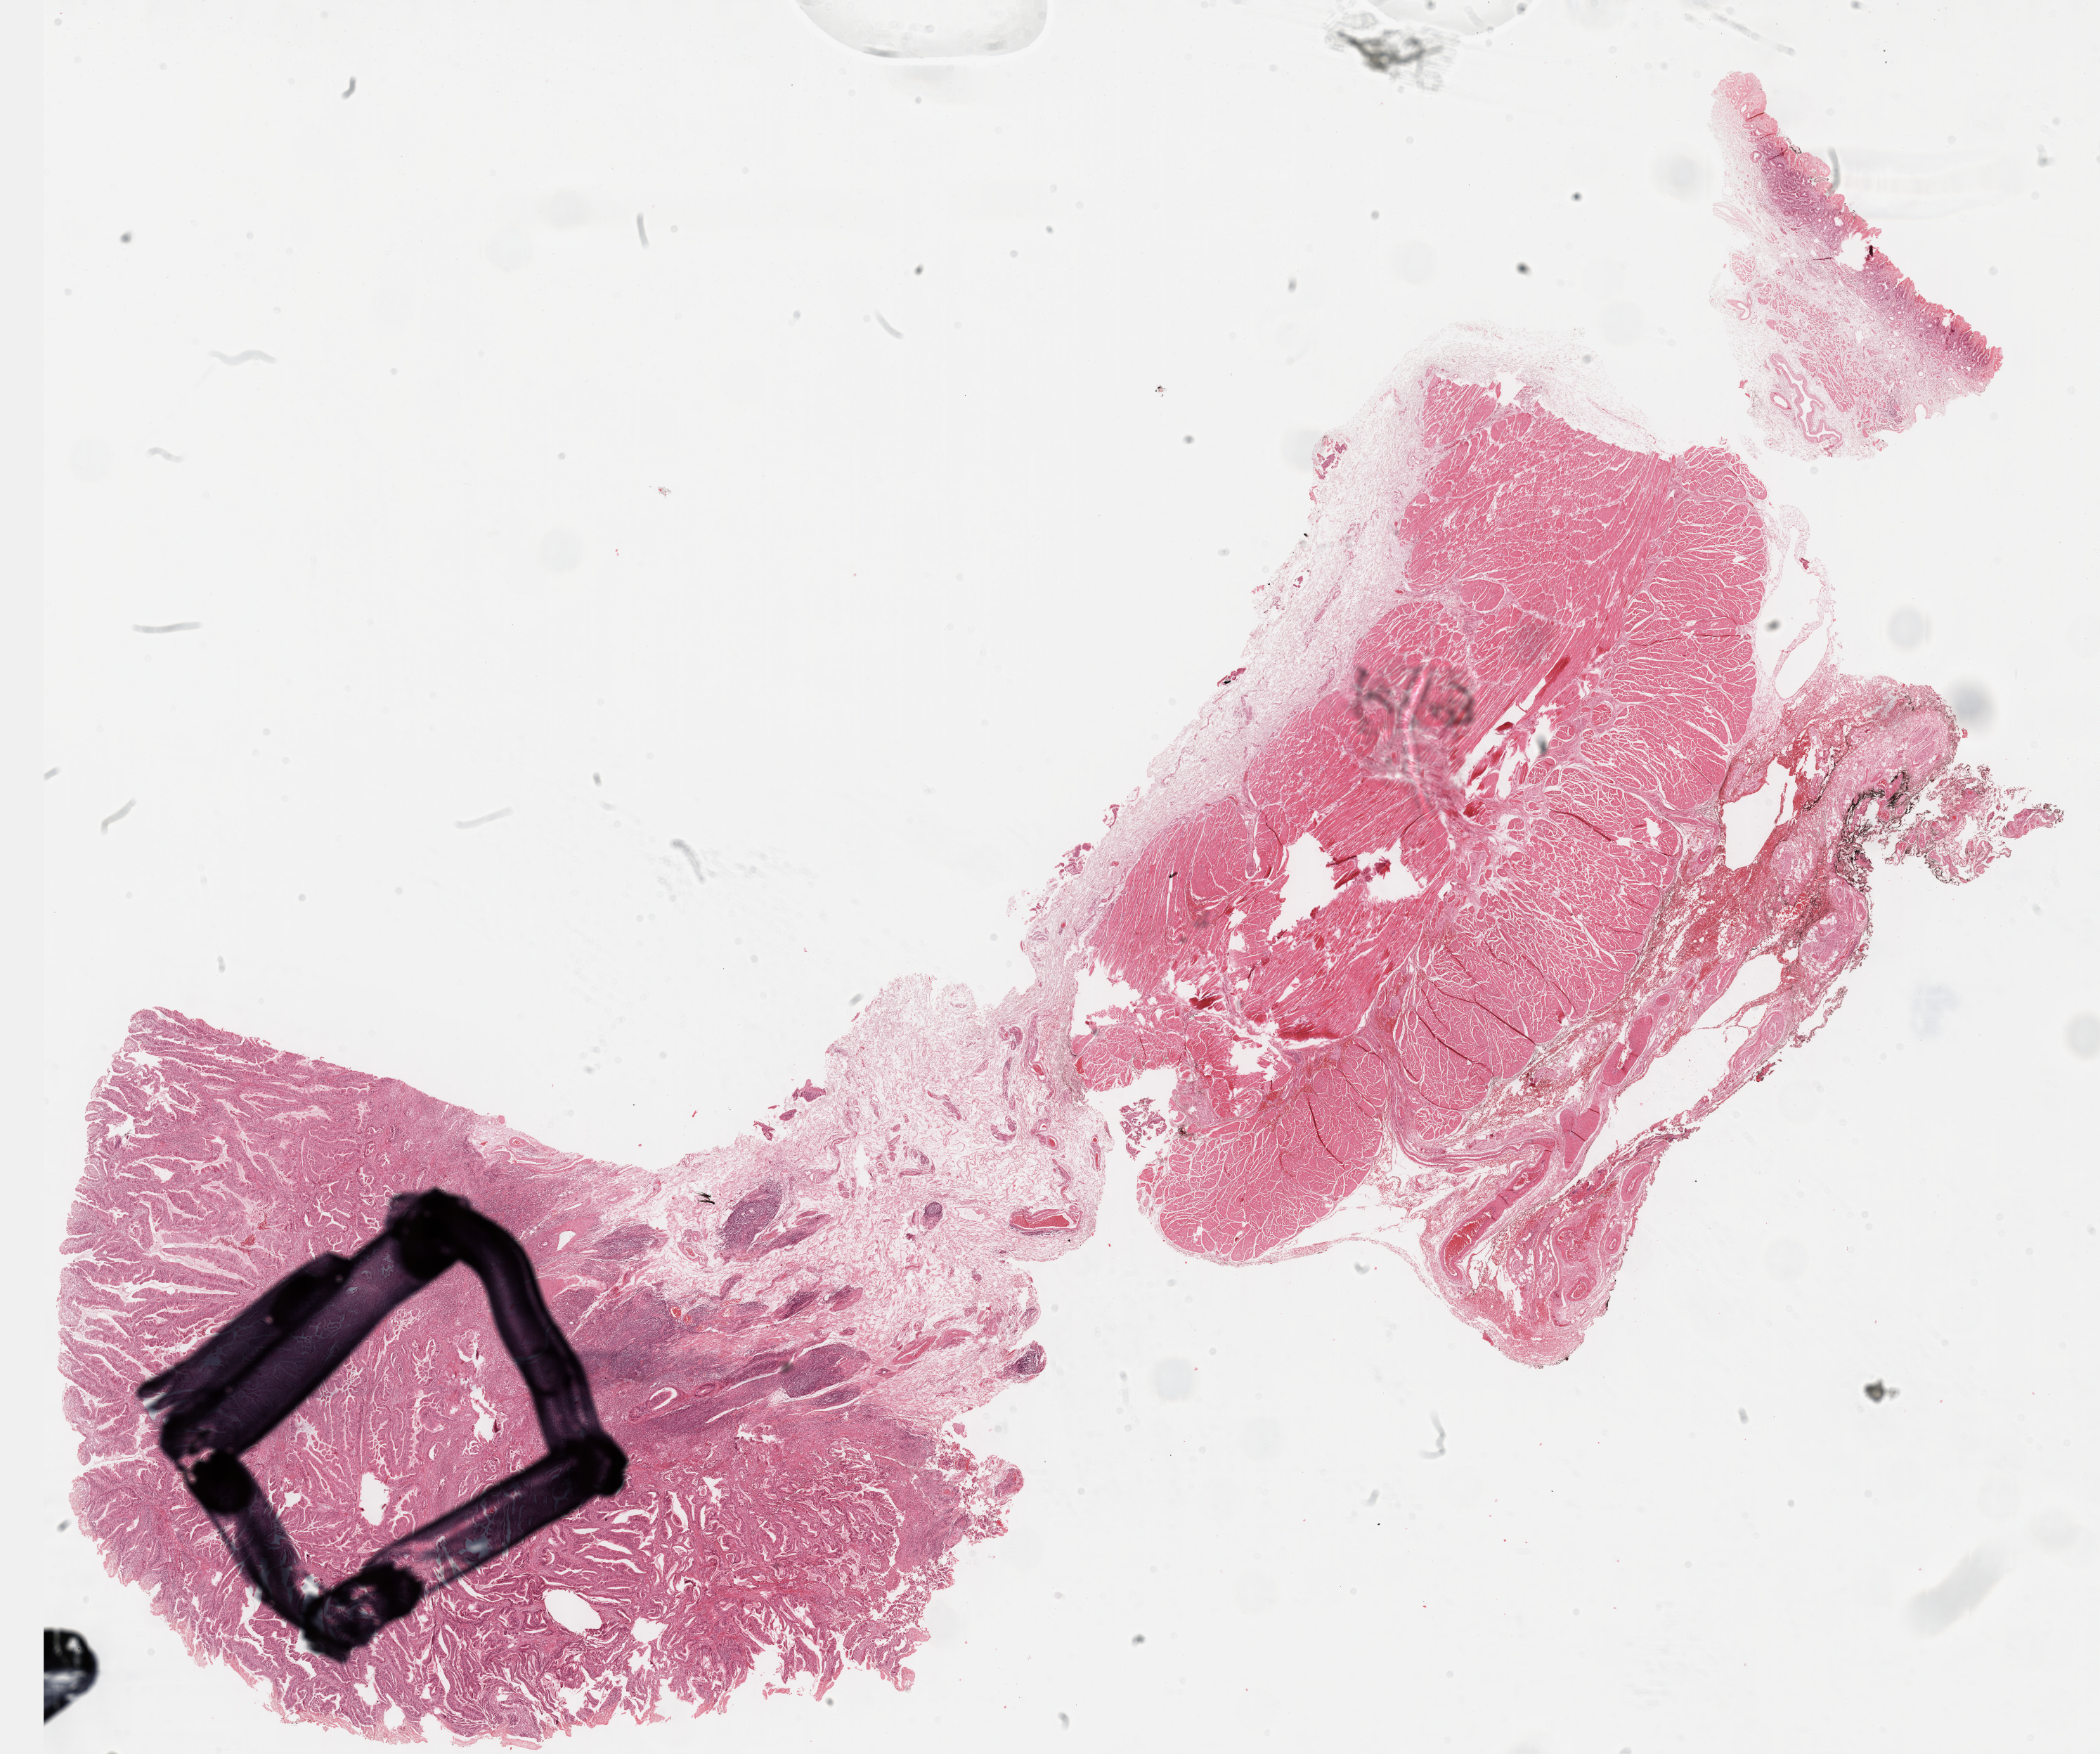
Whole-slide histology image, H&E, low-resolution overview of the scanned area, about 24.1 x 20.2 mm; formalin-fixed paraffin-embedded (FFPE) diagnostic section; primary tumour sample from the esophagus. Male, age 44 years at initial diagnosis. Histologic grade: G2 (moderately differentiated).
AJCC pathologic stage: IIB (5th edition). Lymph nodes positive (case pathology): 1 of 30 examined. Pathologic diagnosis: Adenocarcinoma, NOS (lower third of esophagus).